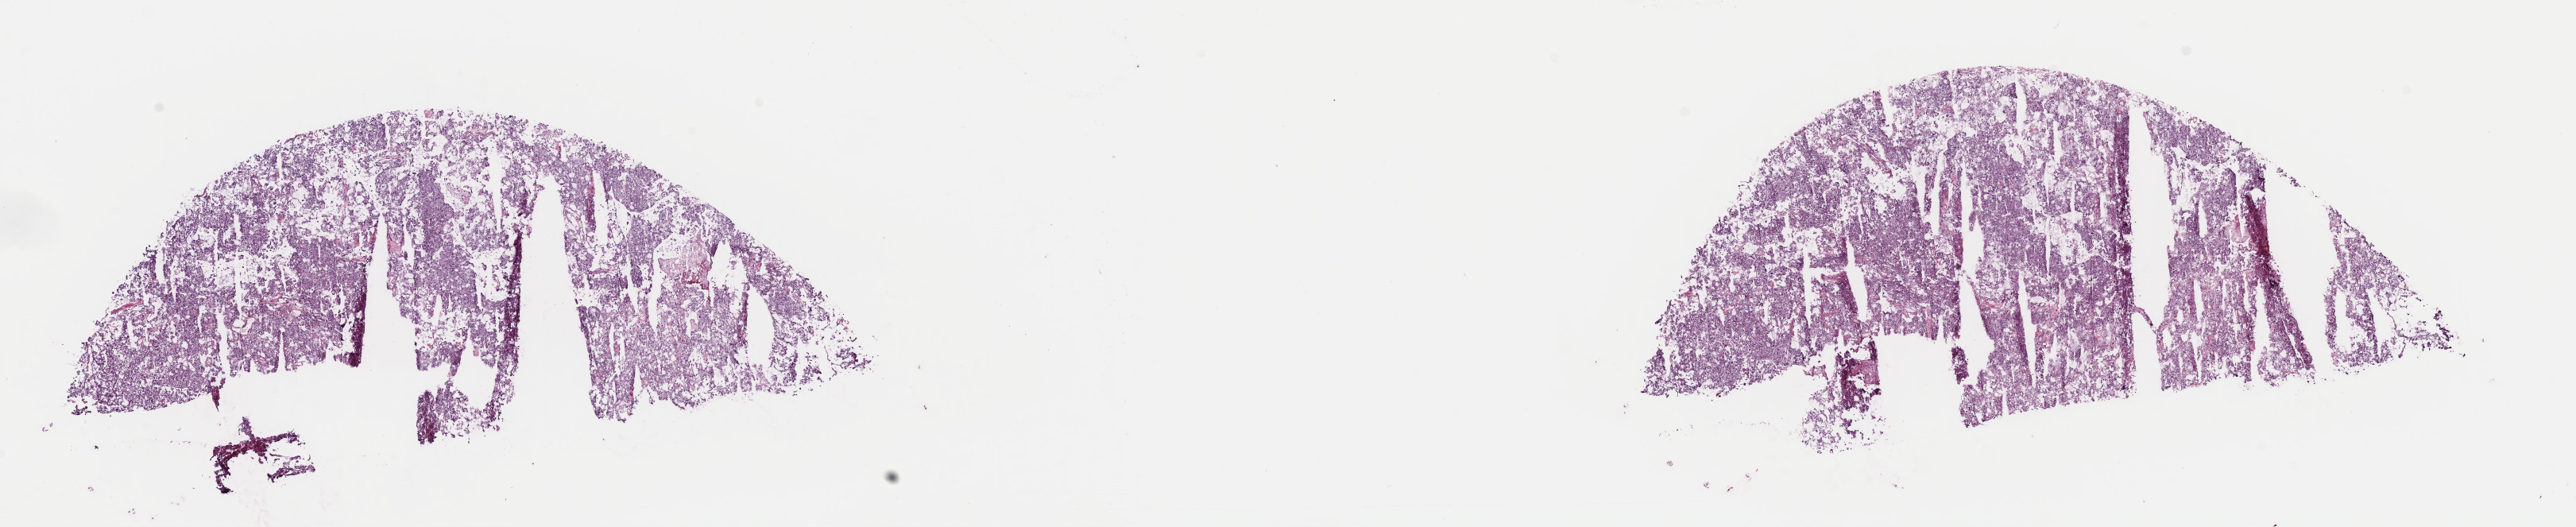
Digitized Hematoxylin and eosin (H&E) stained tissue section (whole slide) — a low-resolution overview of the entire scanned area, about 25.6 x 5.2 mm; frozen section; kidney, primary tumour sample. Male patient; age at initial diagnosis 48 years. Composition of this section per pathologist review: tumour cells 95%, tumour nuclei 95%, normal cells 0%, stromal cells 5%, necrosis 0%. Infiltration values recorded for this section: lymphocyte infiltration 0%, monocyte infiltration 0%, neutrophil infiltration 0%.
AJCC pathologic stage: III. Diagnosis: Renal cell carcinoma, chromophobe type. Laterality: right. TNM: T3a NX.